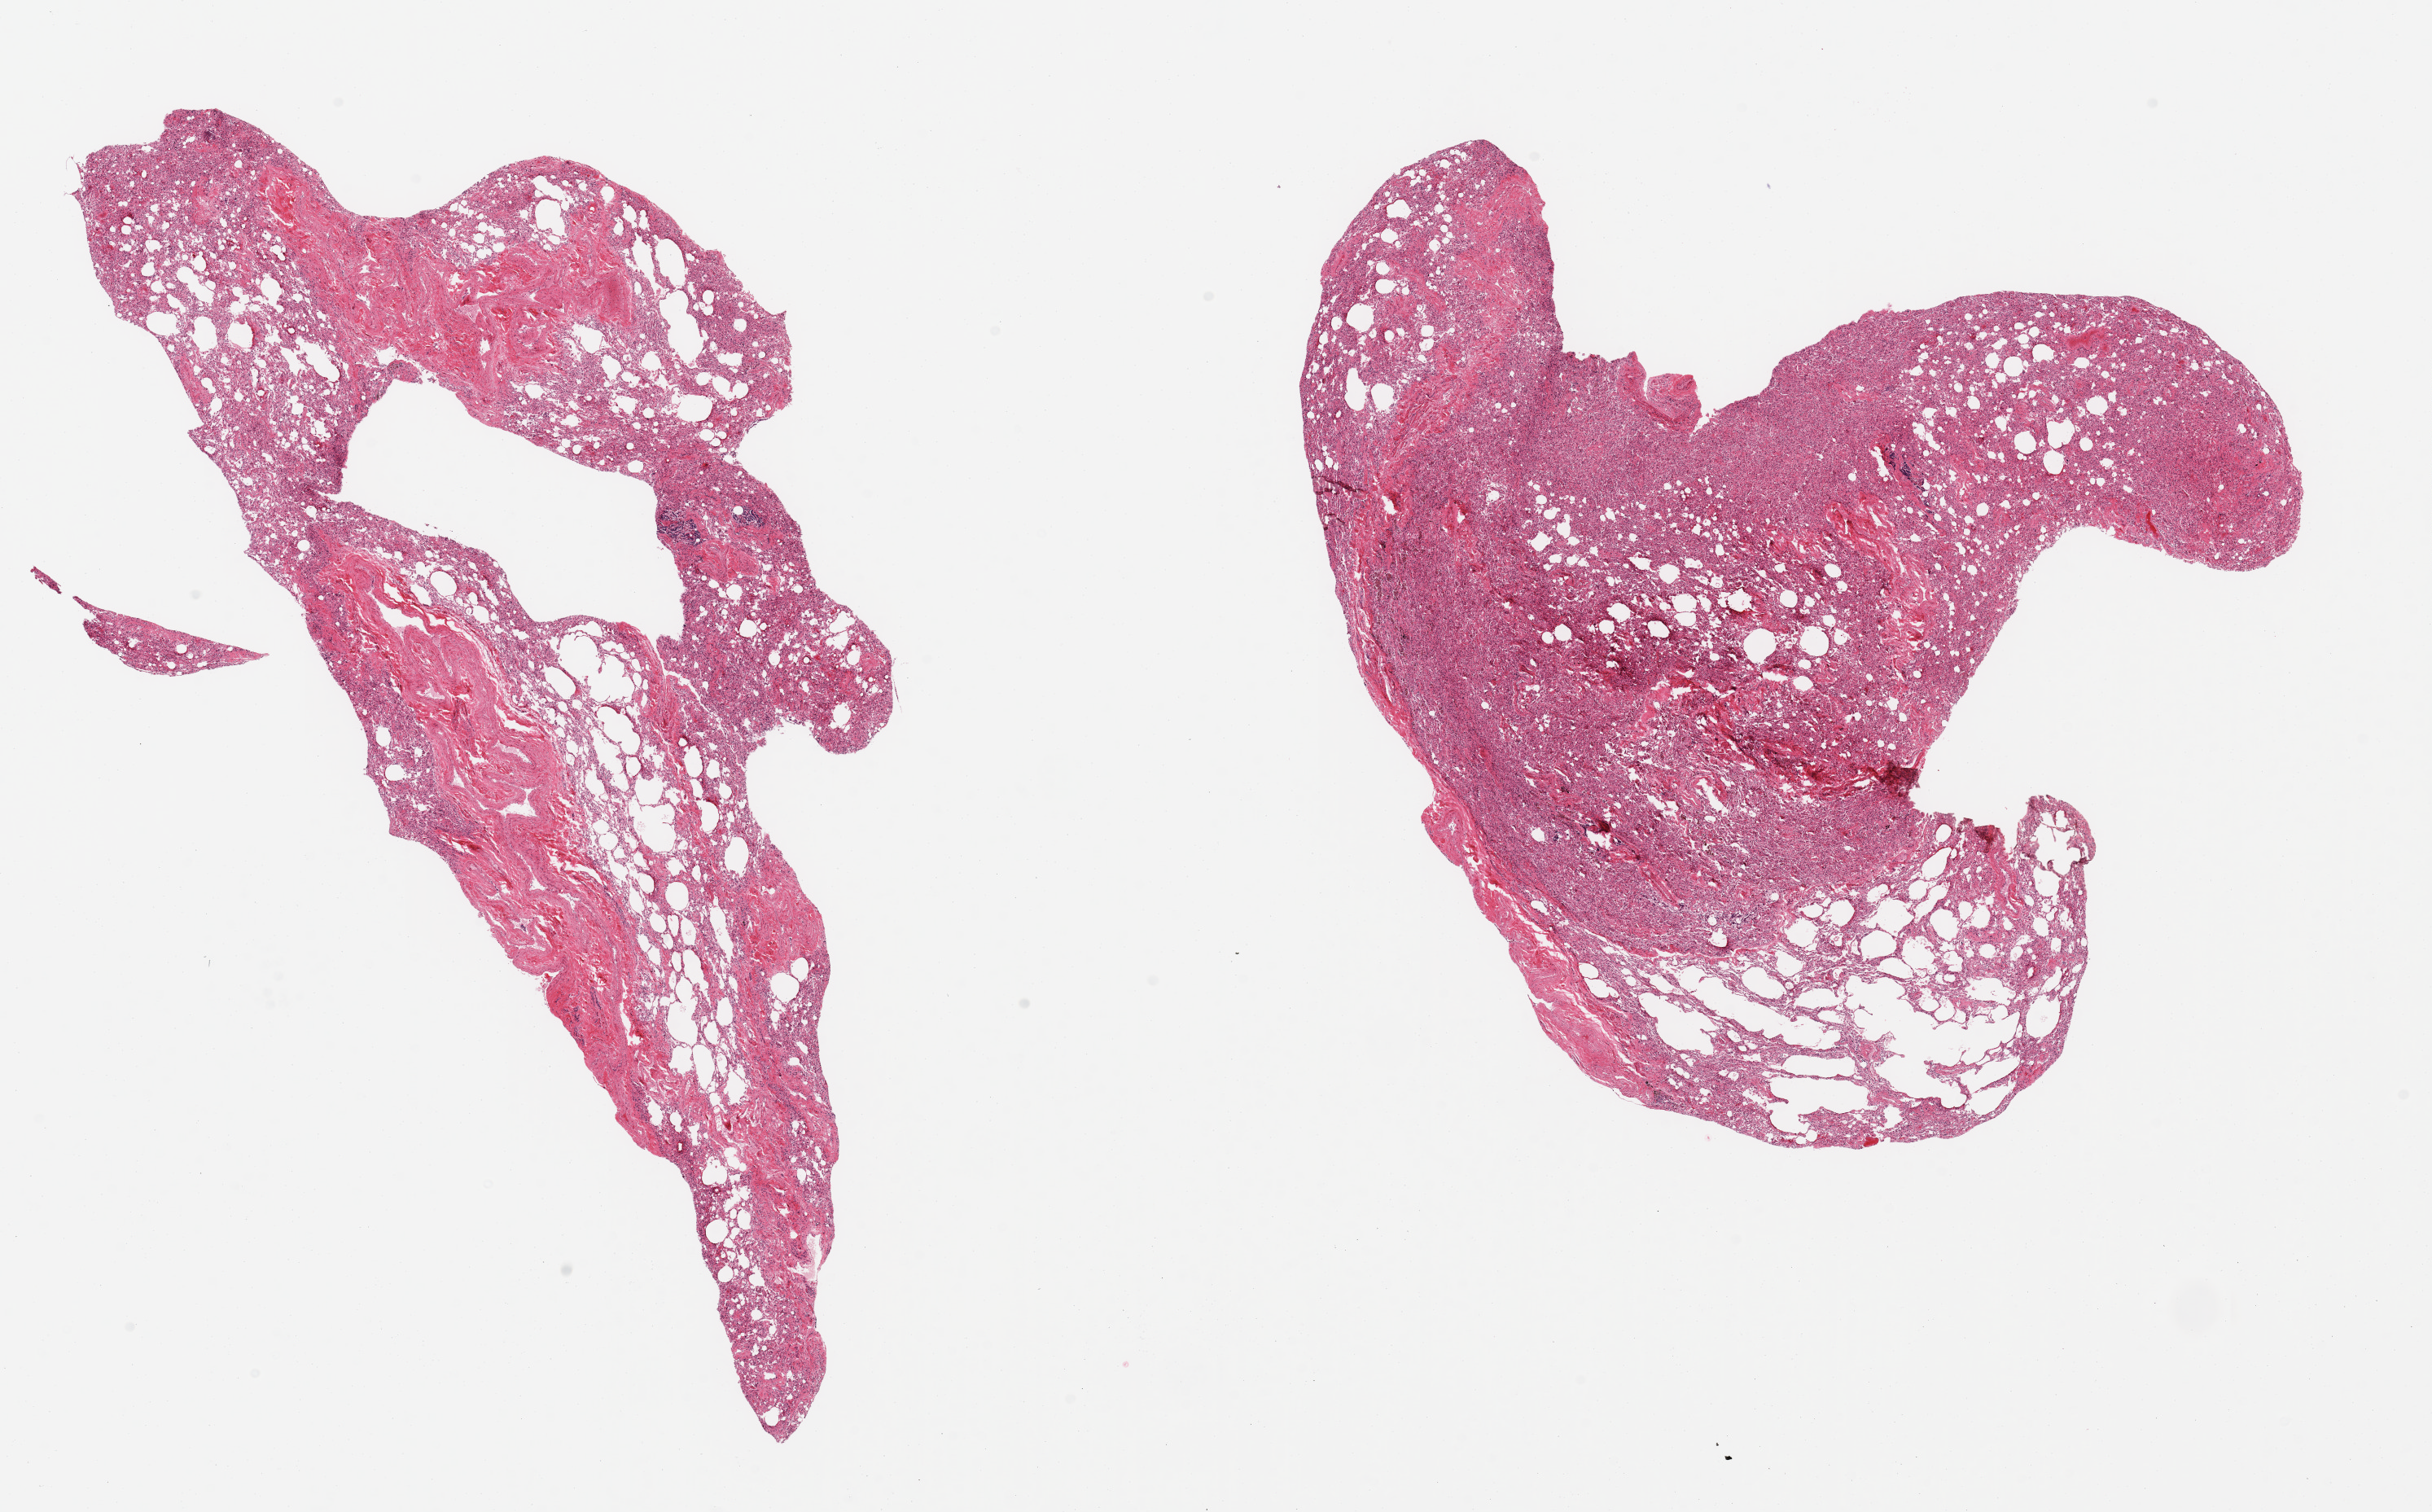
Whole-slide image, H&E stain, low-resolution overview of the scanned area, about 23.6 x 14.7 mm (slide scanned at 20x), PAXgene-fixed paraffin-embedded (PFPE) section, target tissue: lung, tissue donor sample. Male donor.
Pathologist's review note for this sample: 2 pieces, atalectasis, interstitial fibrosis/patchy hyaline membrane formation suggests component of diffuse alveolar damage.